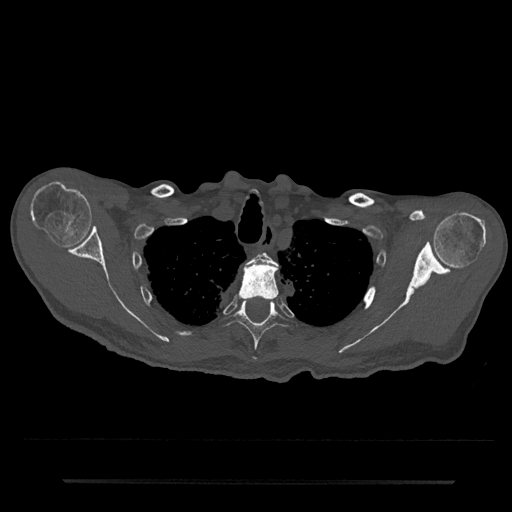
CT including the spine, one axial slice. Reconstruction kernel Br40s/3. Bone window (W 1800 / L 400 HU). 0.5 mm slice thickness. 512 × 512 image matrix. Male patient, age 74 years. Case-level facts recorded for this patient, not image findings: primary cancer: prostate.
Outlined on this slice (semi-automatically segmented with operator editing):
- T2 vertebra: bounding box <245,253,277,268> (left, top, right, bottom; pixels)
- T3 vertebra: <239,262,279,301>
- T4 vertebra: <224,299,288,361>